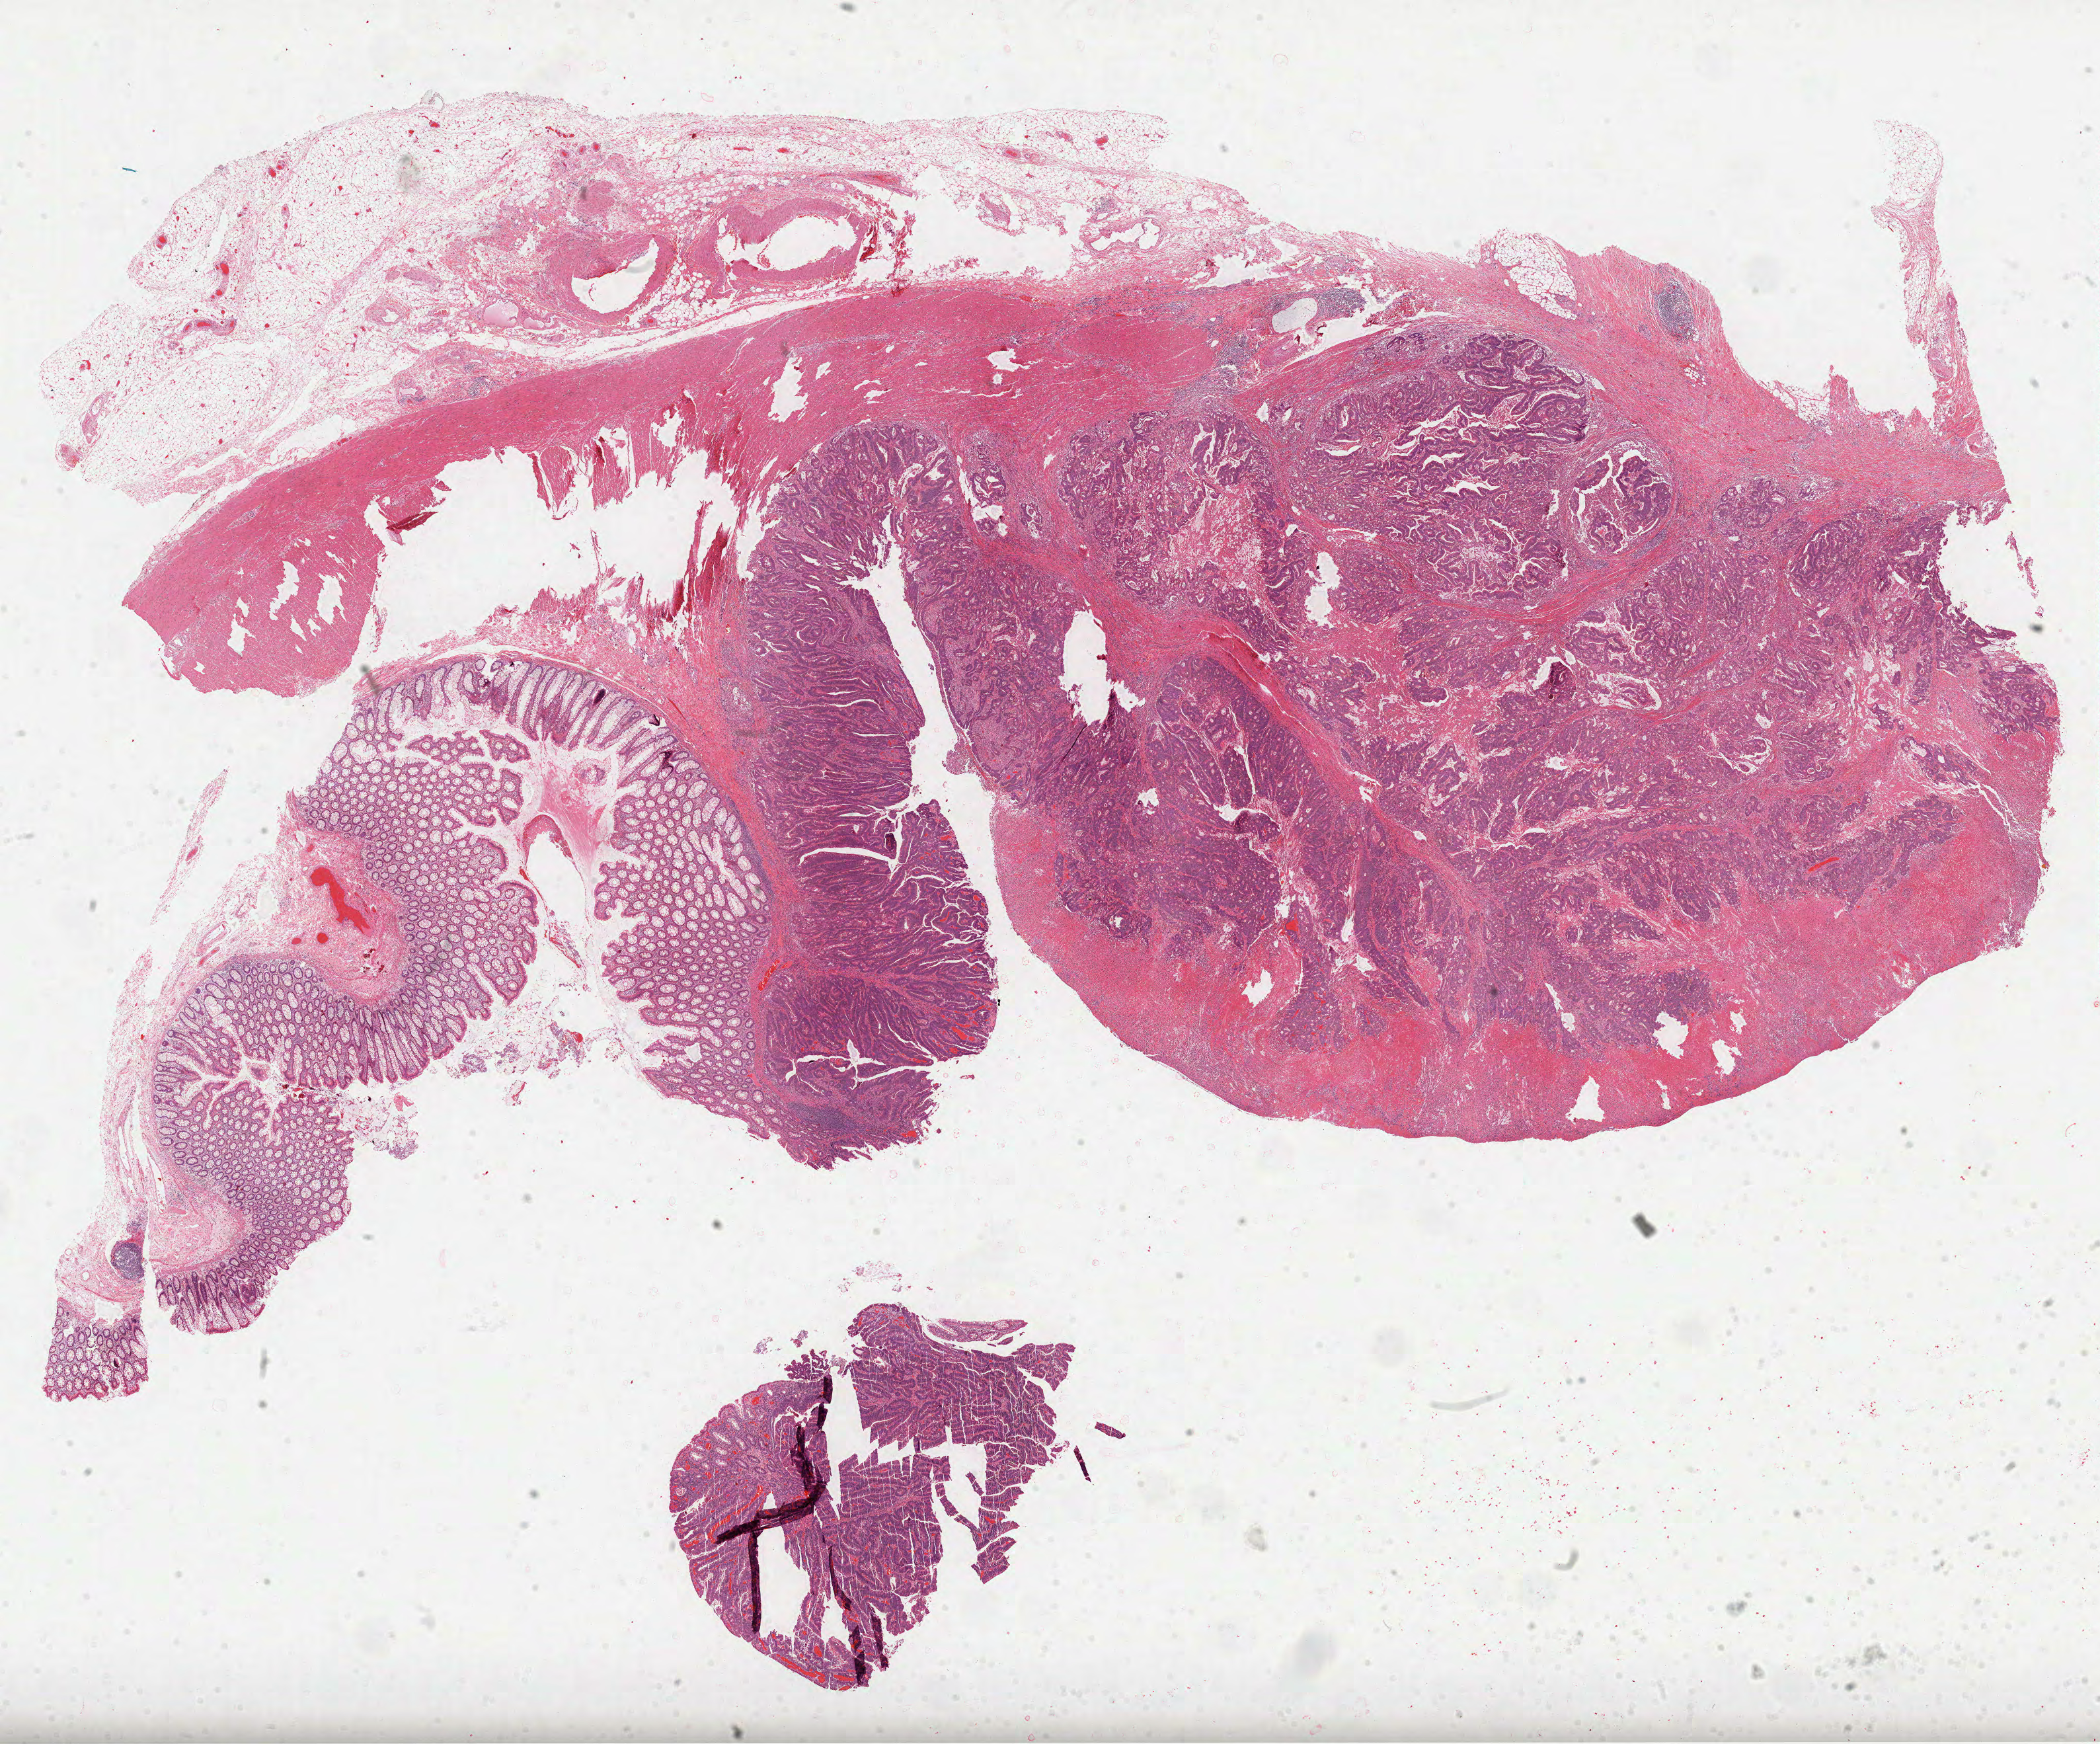
Hematoxylin and eosin (H&E) stained whole-slide image, shown as a low-resolution overview of the whole scanned area (about 25.6 x 21.3 mm, from a 40x scan), FFPE section, colon, primary tumour sample. Patient: male, age at initial diagnosis 68 years.
AJCC pathologic stage: II (5th edition). Pathologic diagnosis: Adenocarcinoma, NOS (sigmoid colon). Lymph nodes positive (case pathology): 0 of 11 examined.